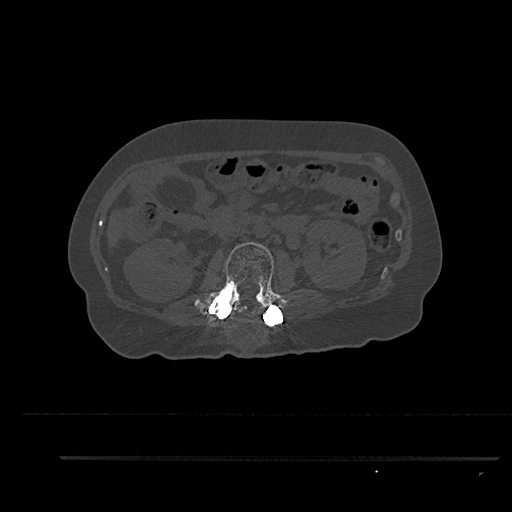
CT including the spine, one axial slice. Reconstruction kernel Br40s/3. 120 kVp. Bone window (W 1800 / L 400 HU). 0.5 mm slice thickness. 512 × 512 image matrix. Patient: female, 44 years. From the clinical record (not read from this slice): primary cancer: renal.
Annotated regions visible in this slice (semi-automatic segmentation, software-assisted and operator-edited):
- L2 vertebra: bounding box (x1, y1, x2, y2) in pixels: (194, 242, 285, 320)